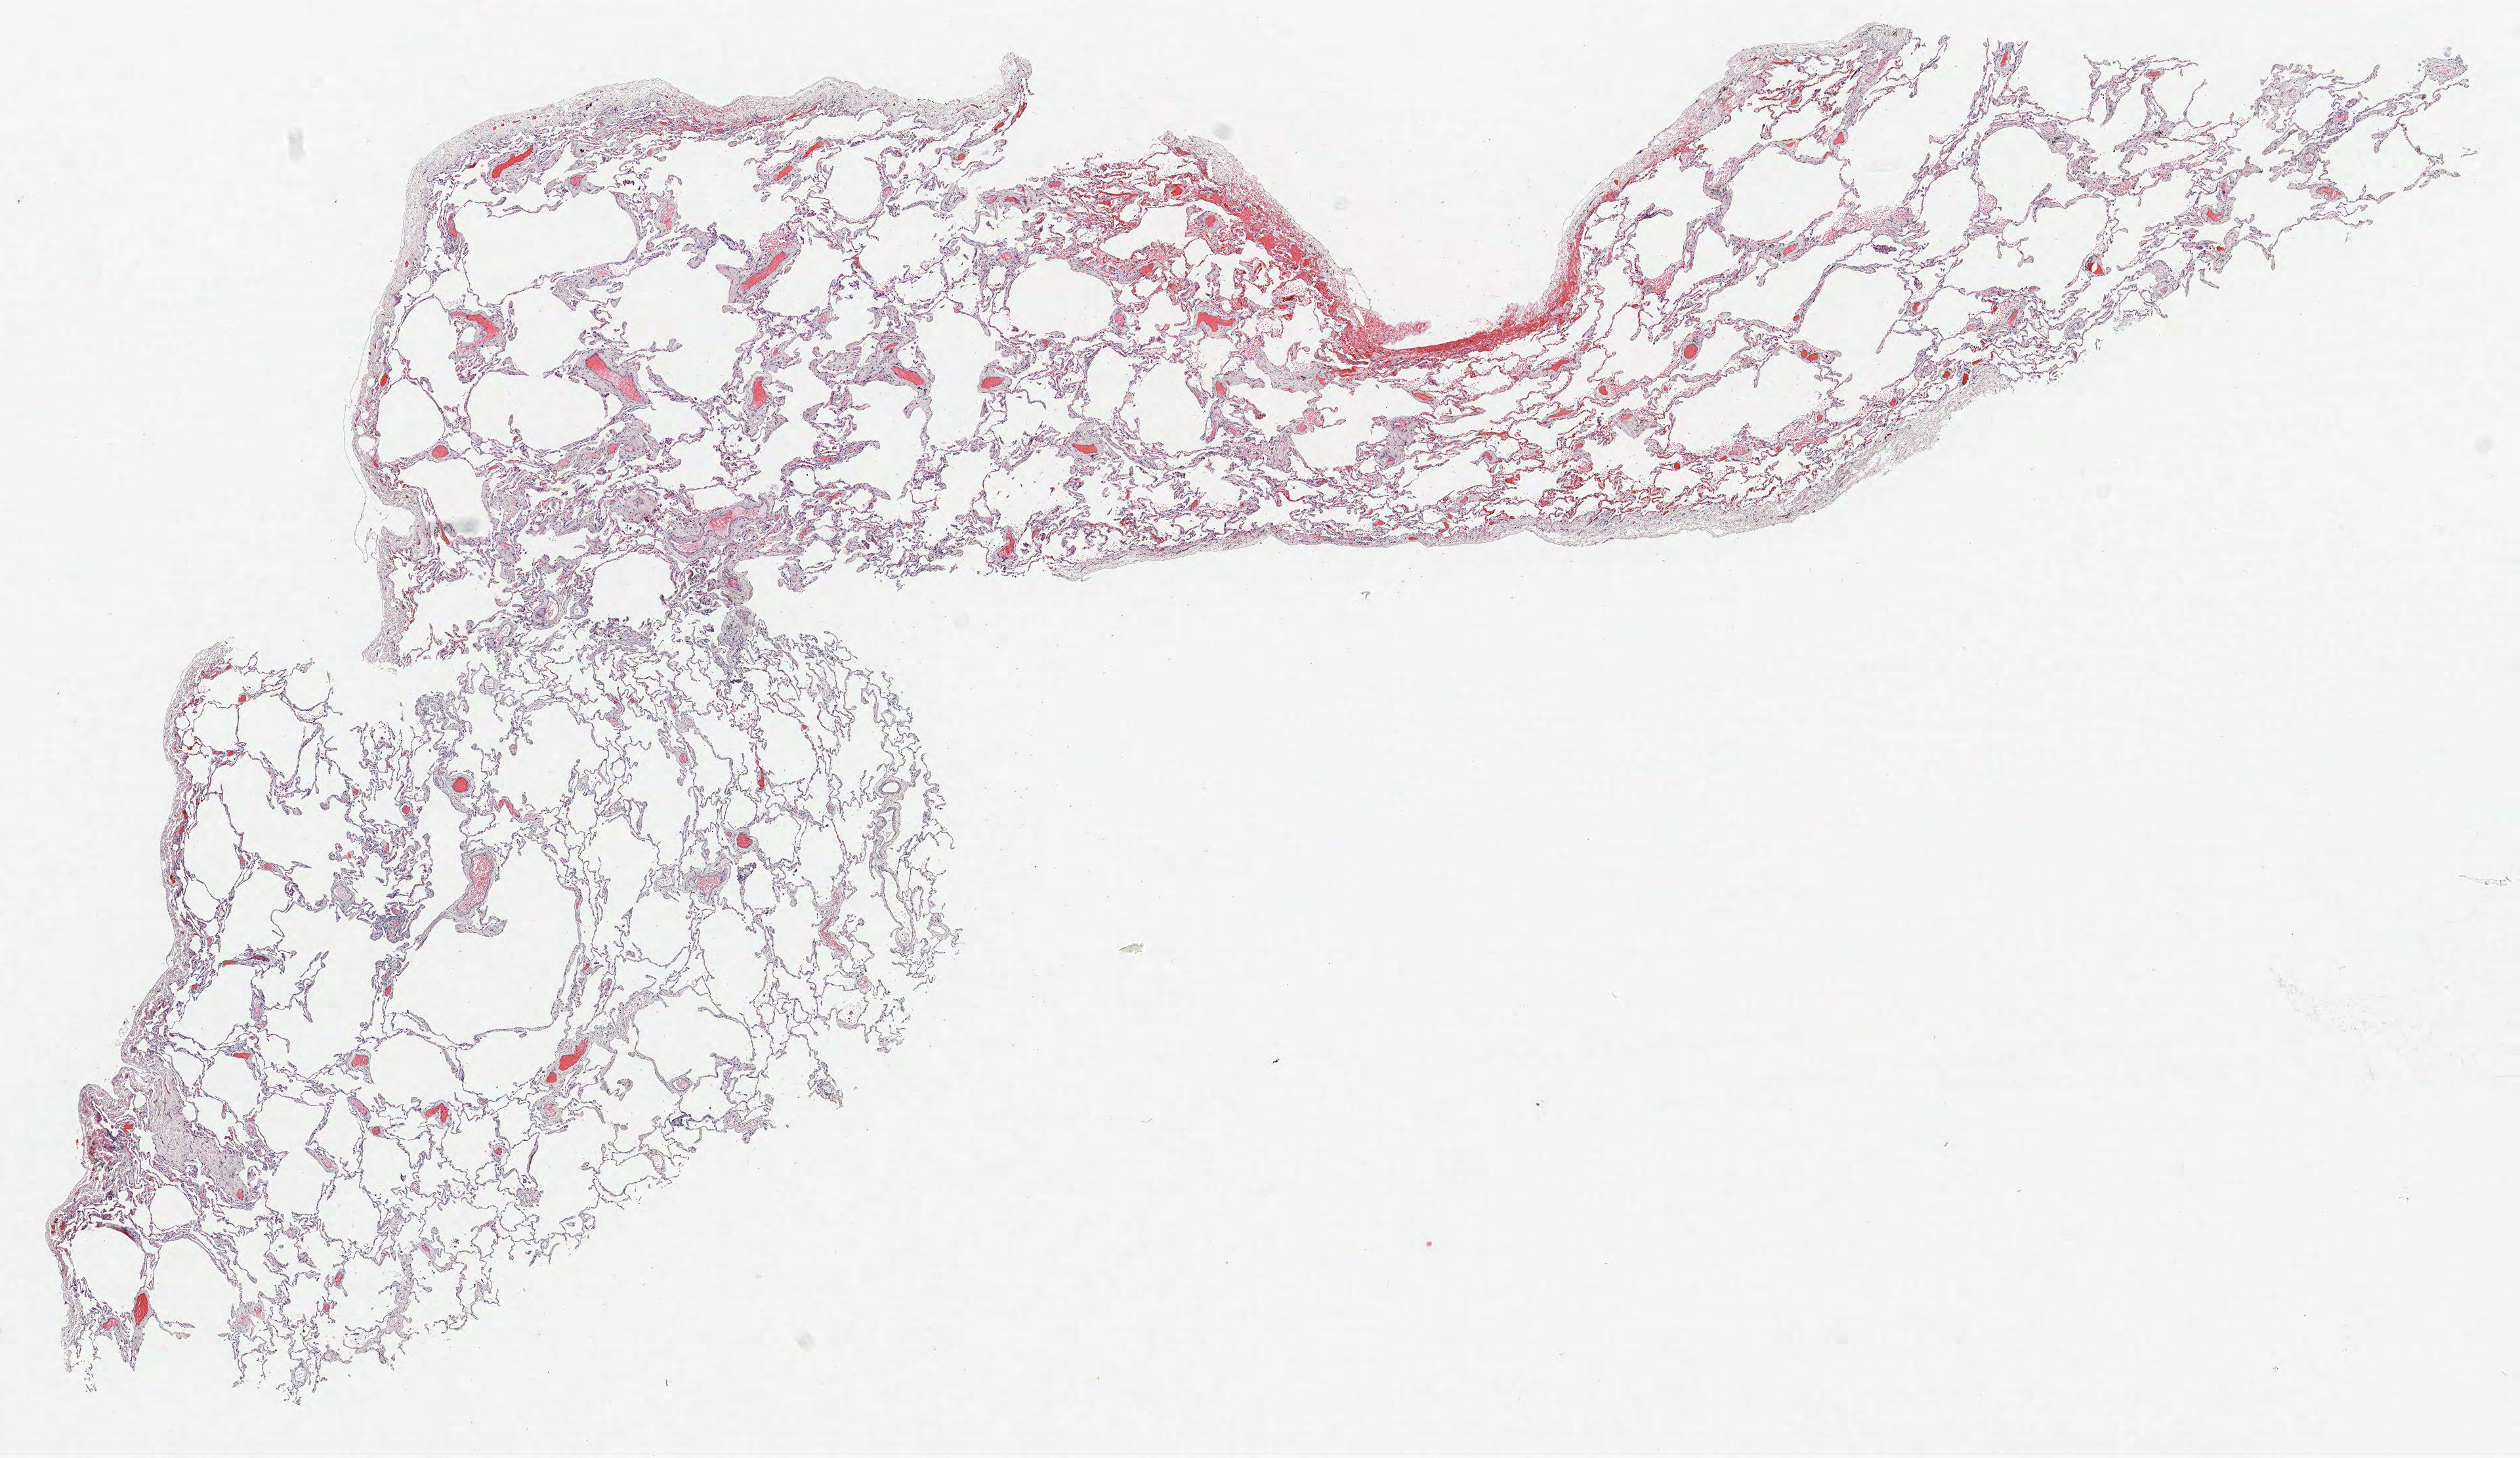
Whole-slide histology image, Hematoxylin and eosin (H&E) stained — a low-resolution overview of the entire scanned area, about 15.4 x 8.9 mm (slide scanned at 40x). Formalin-fixed paraffin-embedded (FFPE) section. Lung tissue. Female patient, aged 64 at enrolment. Current smoker at enrolment. Grade: moderately differentiated (G2).
• stage (AJCC 6th edition): IA
• primary tumour location (clinical record): right lower lobe
• tumour size (pathology): 15 mm
• participant's lung-cancer diagnosis: Adenocarcinoma, NOS (ICD-O-3 8140/3)